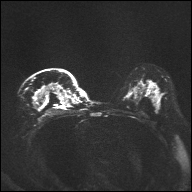
Breast MRI, one axial slice. Position 22 of 32 along the scan axis. Diffusion-weighted series; image 2 of 4 stored at this slice position (different b-values; order by instance number). 1.5 T. 4 mm slice thickness. 192 × 192 image matrix, field of view 360 × 360 mm. Female patient.
Annotated regions visible in this slice (outlined manually by an expert reader):
- tumour on diffusion-weighted imaging: bounding box [x1, y1, x2, y2] px = [39, 86, 53, 99]